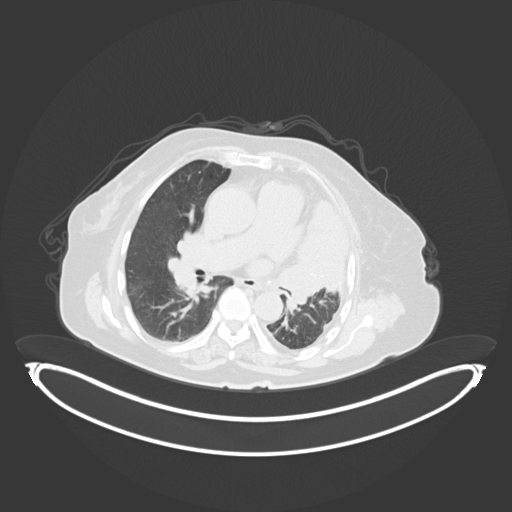
Chest CT, one axial slice. Slice 198 of 284 in the series (ordered by position). Reconstruction kernel B30f. Lung window (W 1500 / L -600 HU). 3 mm slice thickness. 512 × 512 image matrix. Patient: female, 75 years. From the clinical record (not read from this slice): clinical TNM (as recorded): T3 N3 M1.
Outlined on this slice (rectangle marked by the reading radiologist):
- lung tumour (recorded histology: adenocarcinoma): bounding box <279,195,355,310> (left, top, right, bottom; pixels)